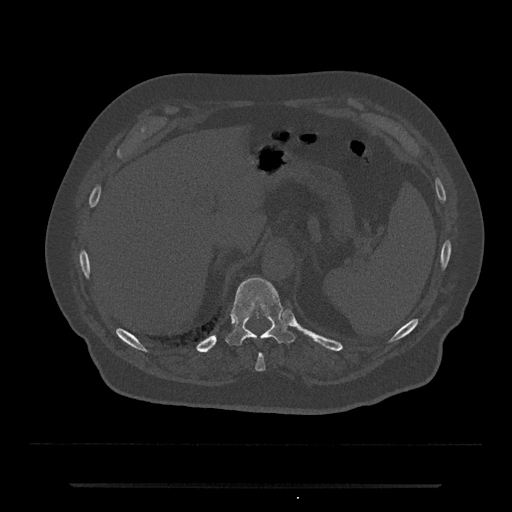
CT including the spine, one axial slice; slice 660 of 797 in the series (ordered by position); 120 kVp; bone window (W 1800 / L 400 HU); 0.5 mm slice thickness; 512 × 512 image matrix, field of view 434 × 434 mm. Male patient, age 80 years. From the clinical record (not read from this slice): primary cancer: prostate; vertebrae with lytic lesions (as recorded): L1, T11.
Structures marked on this image (semi-automatic segmentation, software-assisted and operator-edited):
- T10 vertebra: bounding box [x1, y1, x2, y2] px = [255, 354, 266, 371]
- T11 vertebra: [225, 277, 294, 346]